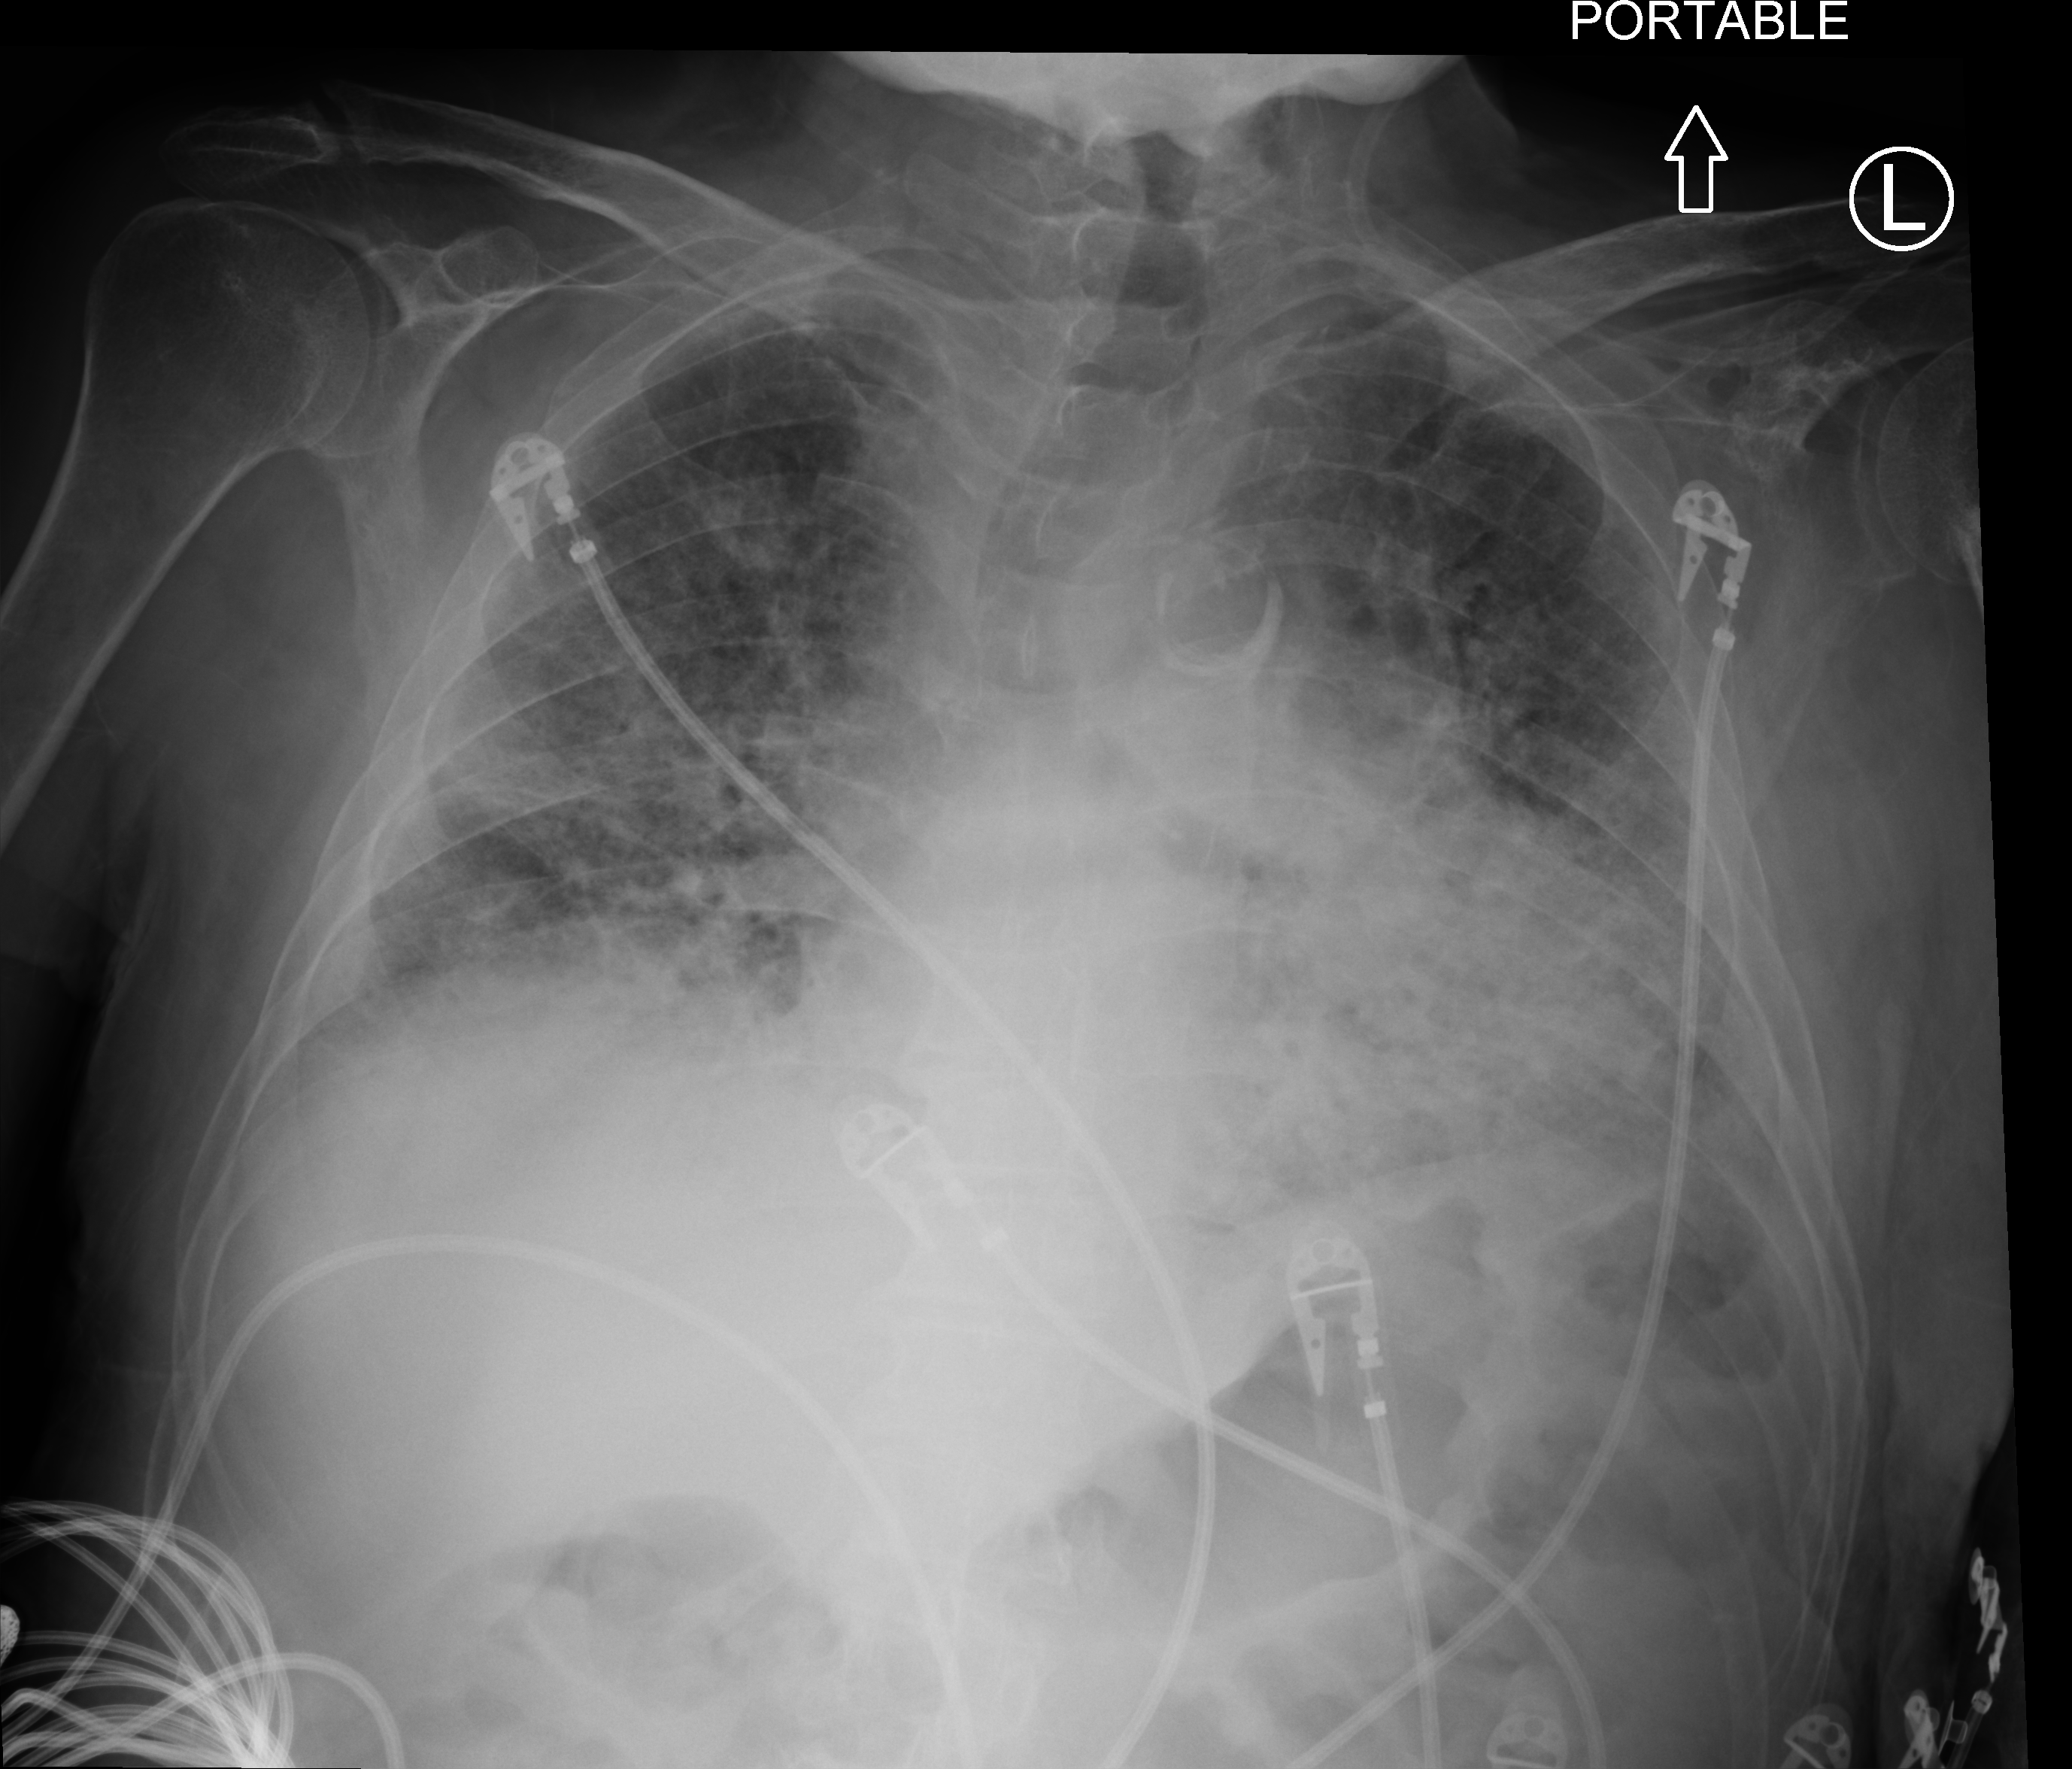
Portable chest radiograph; anteroposterior (AP) projection. Patient hospitalised with COVID-19; male, aged 60–74 years.
Admission-level facts for this patient (not findings on this image; timing relative to this image not recorded):
- hypertension (admission record): yes